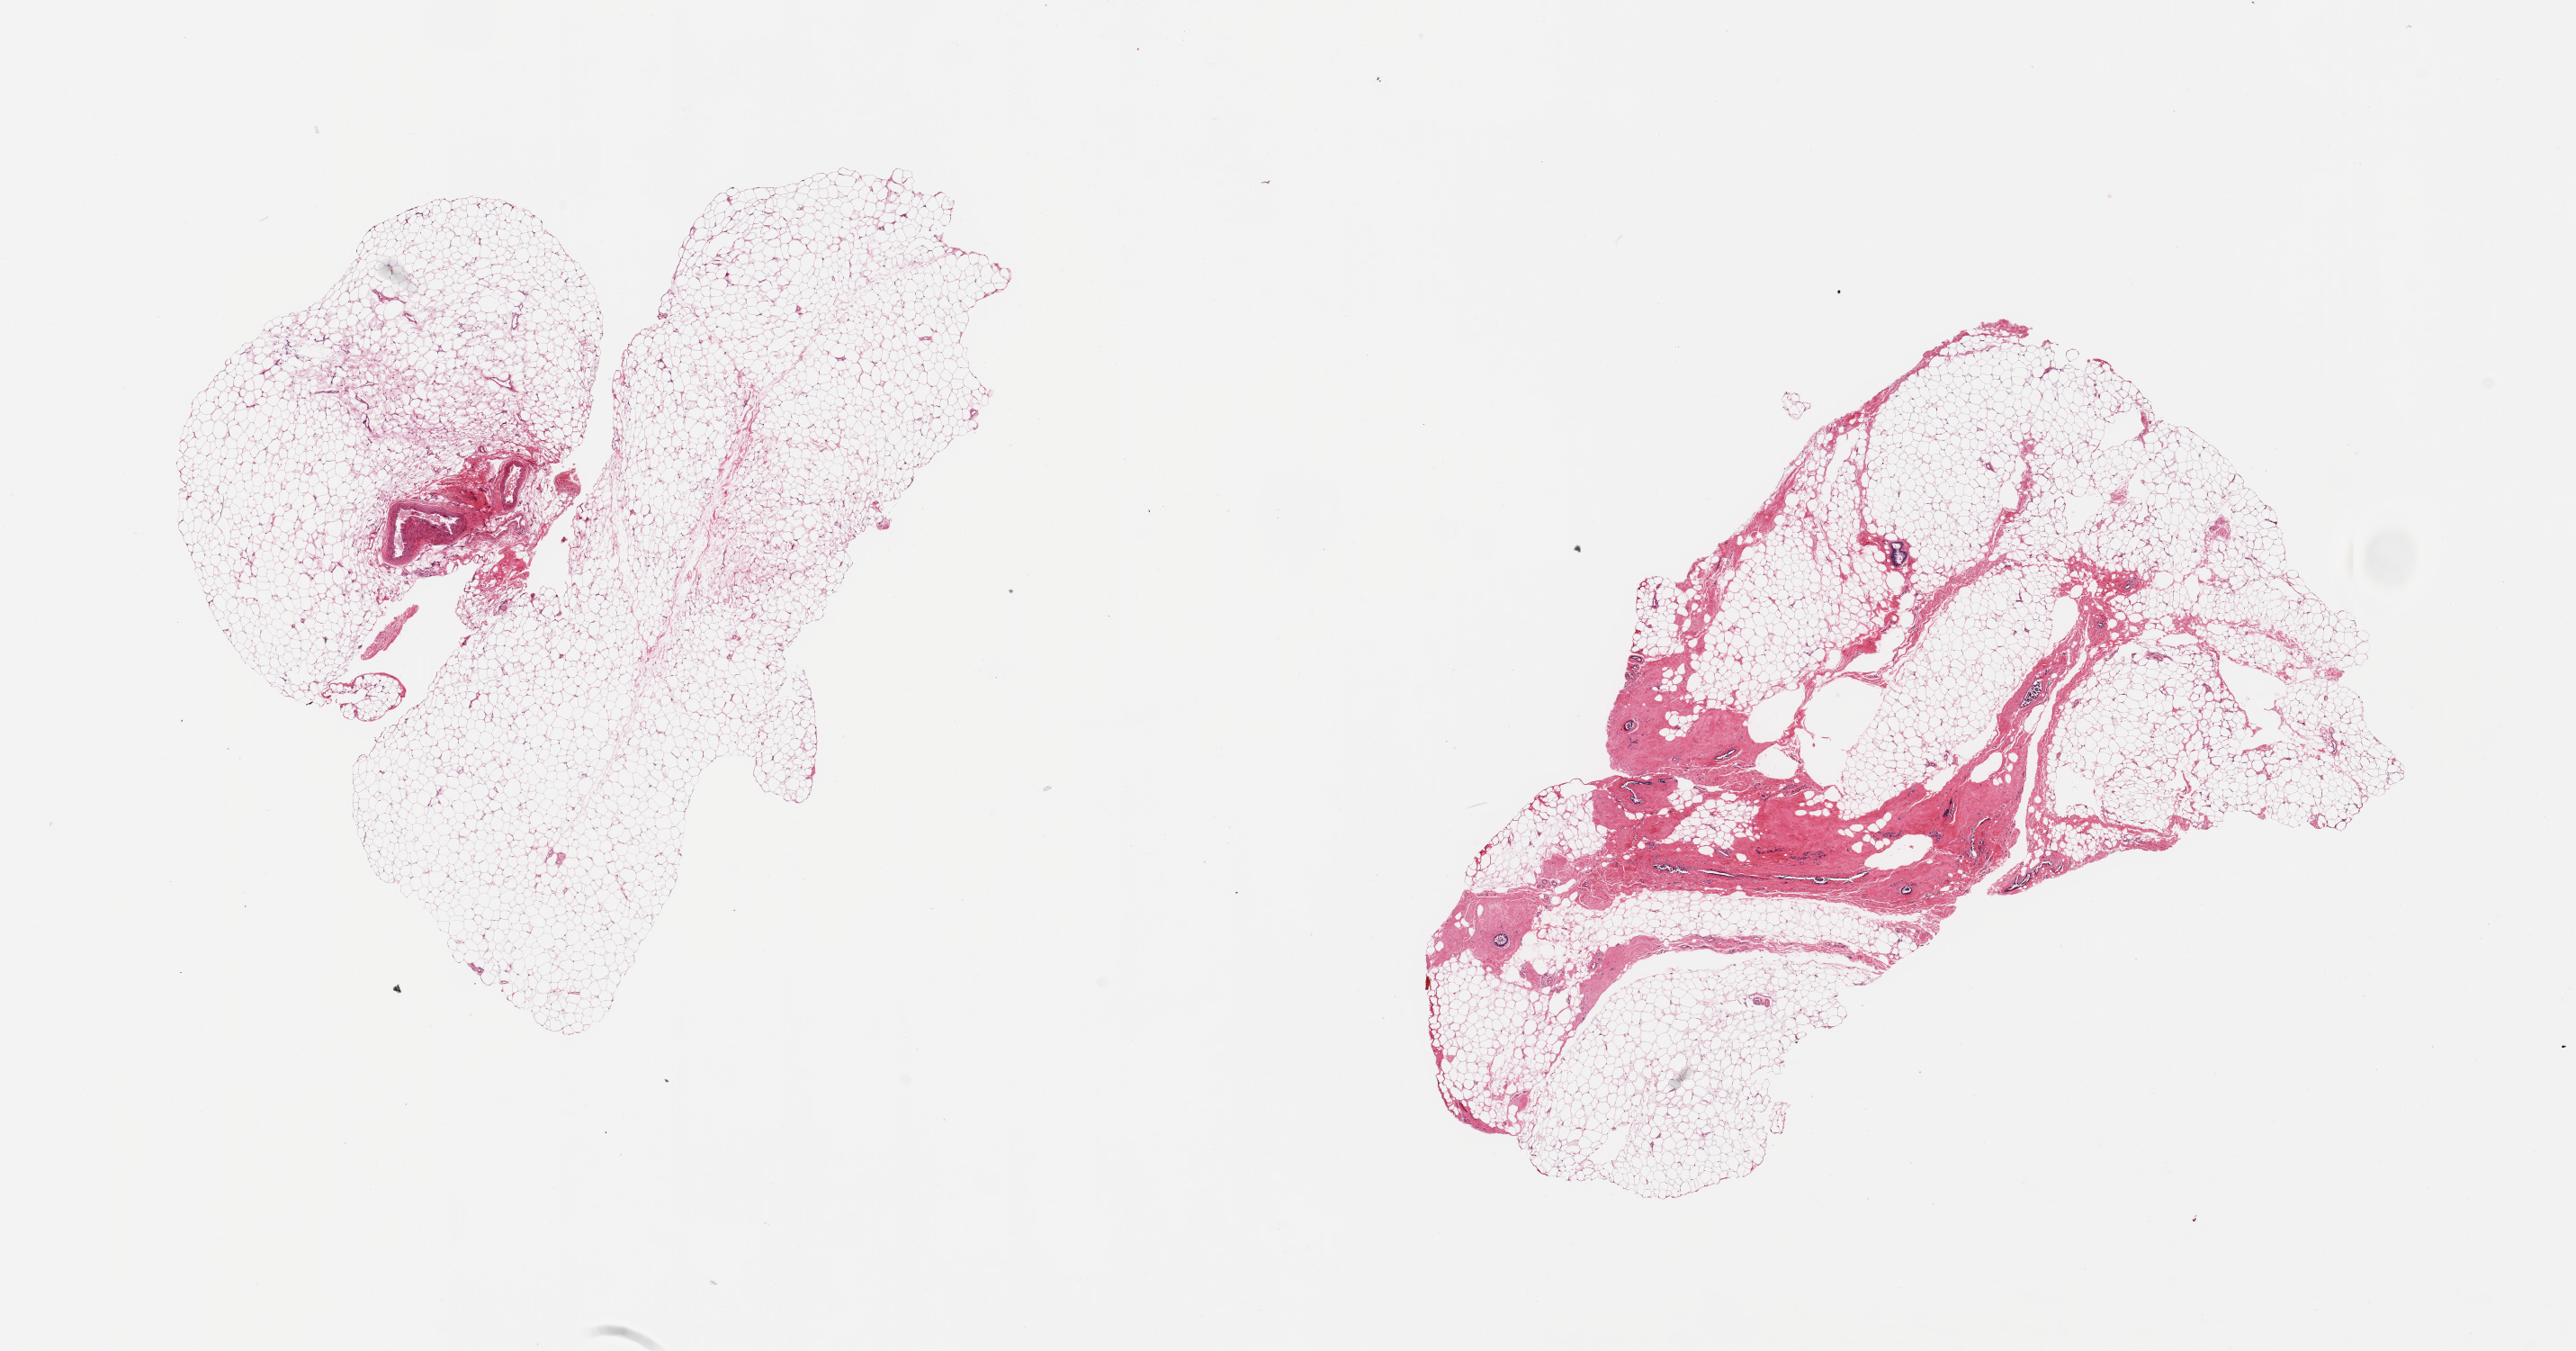
Whole-slide image, haematoxylin and eosin stain, brightfield — low-resolution overview of the scanned area, about 22.6 x 11.9 mm (acquisition: 20x scan). PAXgene-fixed paraffin-embedded (PFPE) section. Sampled site (target tissue): breast. Tissue donor sample. Donor sex: male.
* review note (as recorded): 2 pieces; mammary ducts, moderately autolyzed, in fibroadipose tissue in 1 piece; no ducts in other piece